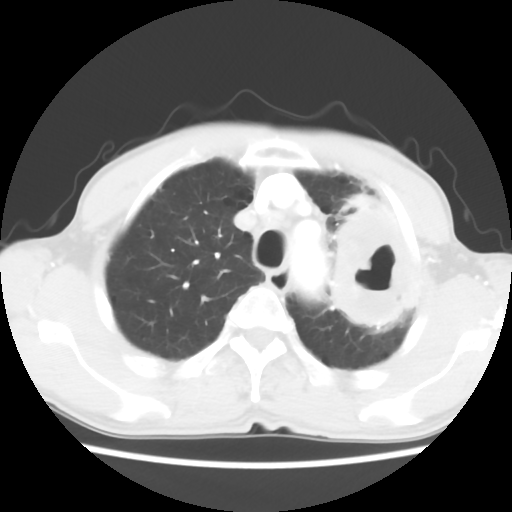
Chest CT, one axial slice; slice 47 of 60 in the series (ordered by position); reconstruction kernel STANDARD; 120 kVp; lung window (W 1500 / L -600 HU); 512 × 512 image matrix, field of view 308 × 308 mm. Patient: male, 64 years. From the clinical record (not read from this slice): clinical TNM (as recorded): T3 N3 M0; histopathological grade: G3.
Outlined on this slice (rectangle marked by the reading radiologist):
- lung tumour (recorded histology: adenocarcinoma): box from (x=328, y=189) to (x=420, y=341) px